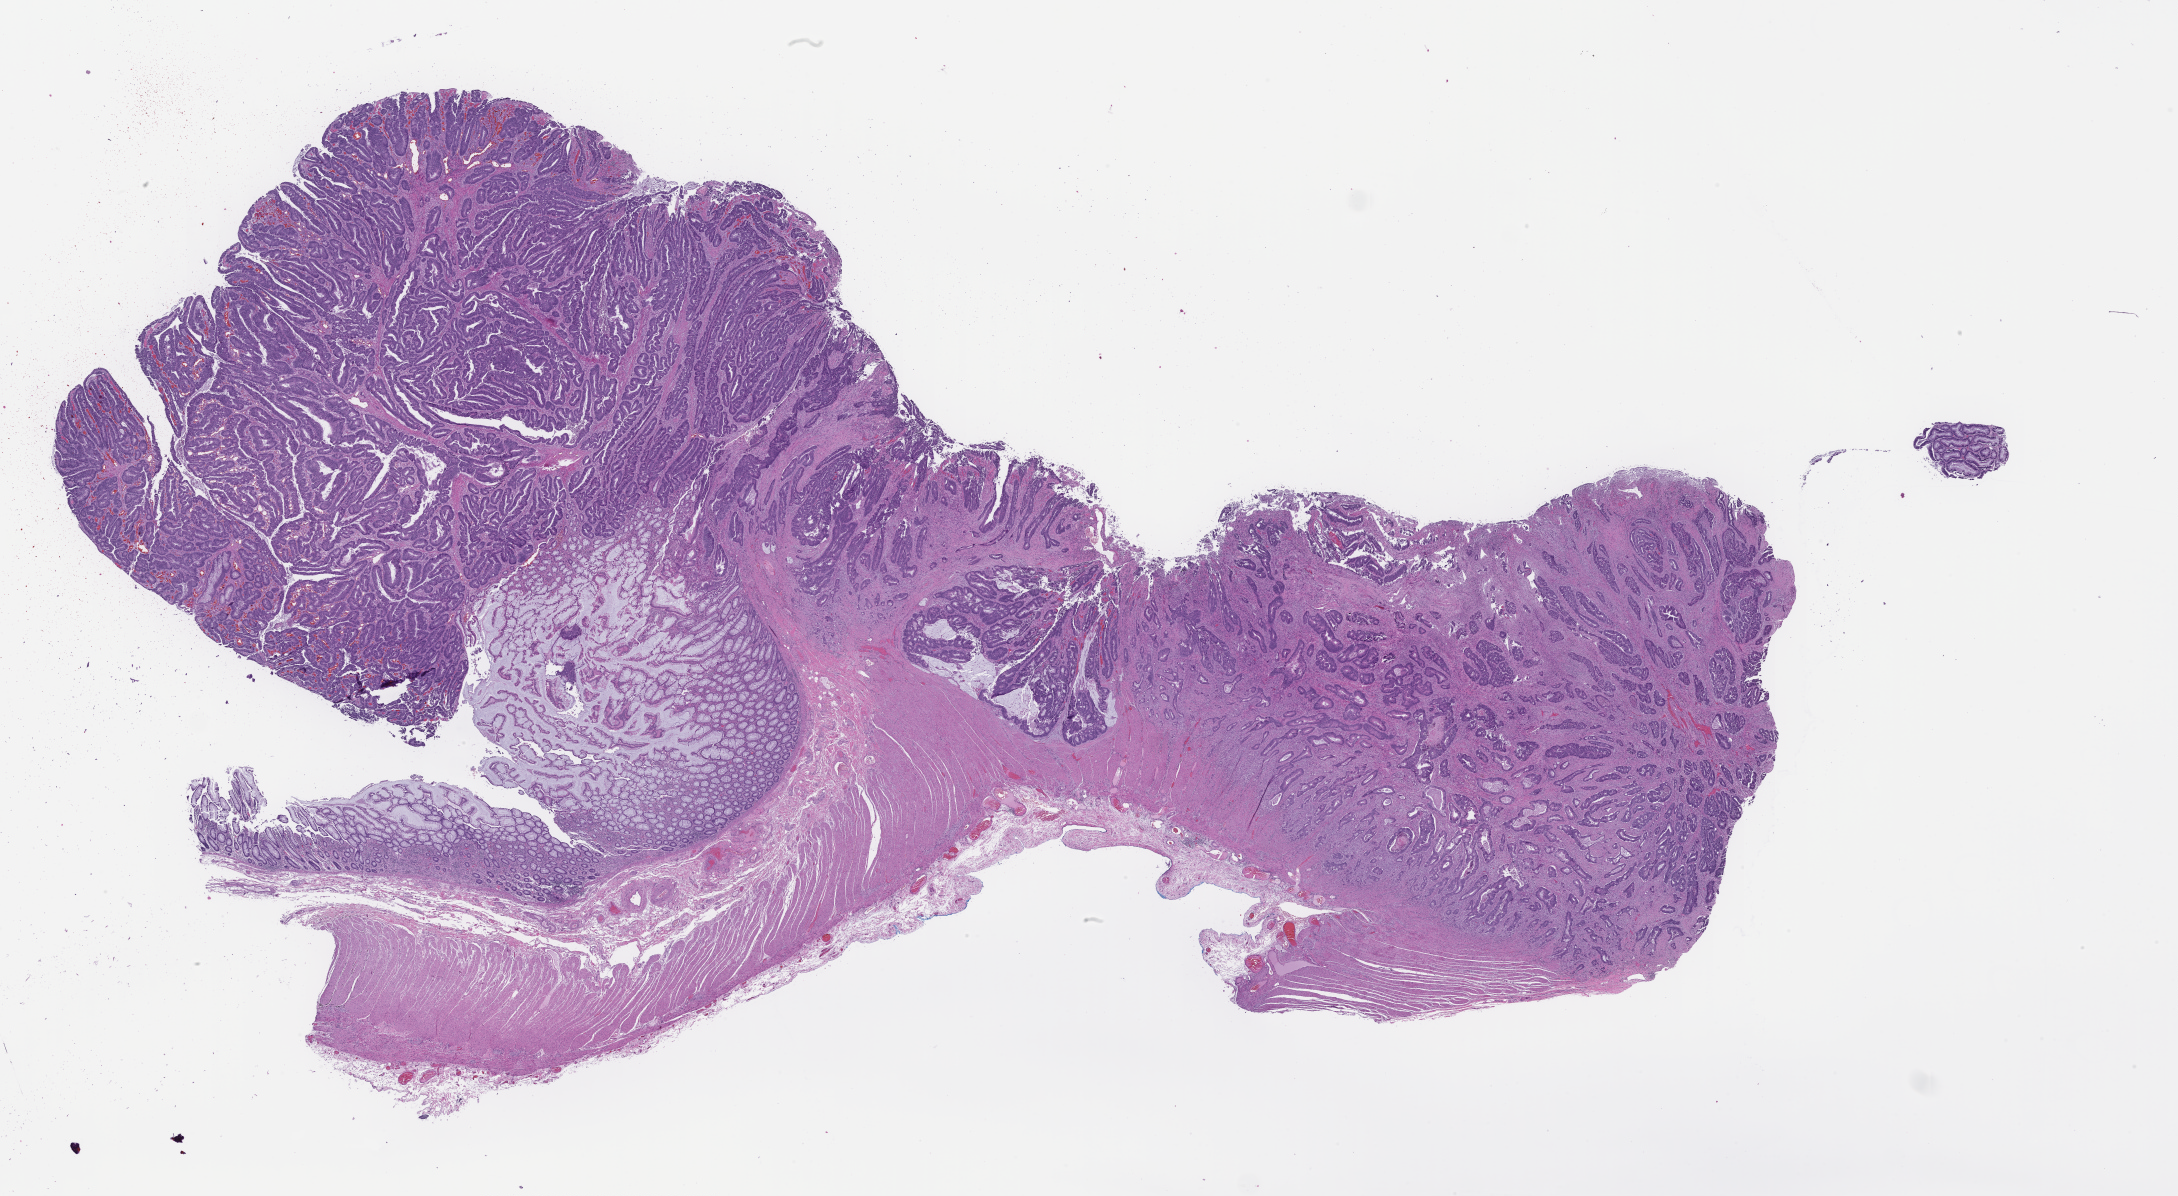
Whole-slide image, hematoxylin and eosin (H&E) stain, whole scanned area (about 35.2 x 19.3 mm) shown as a low-resolution overview; formalin-fixed, paraffin-embedded (FFPE) tissue; site: colon. Patient sex: female.
- this section: primary tumor
- diagnosis: Colorectal Carcinoma